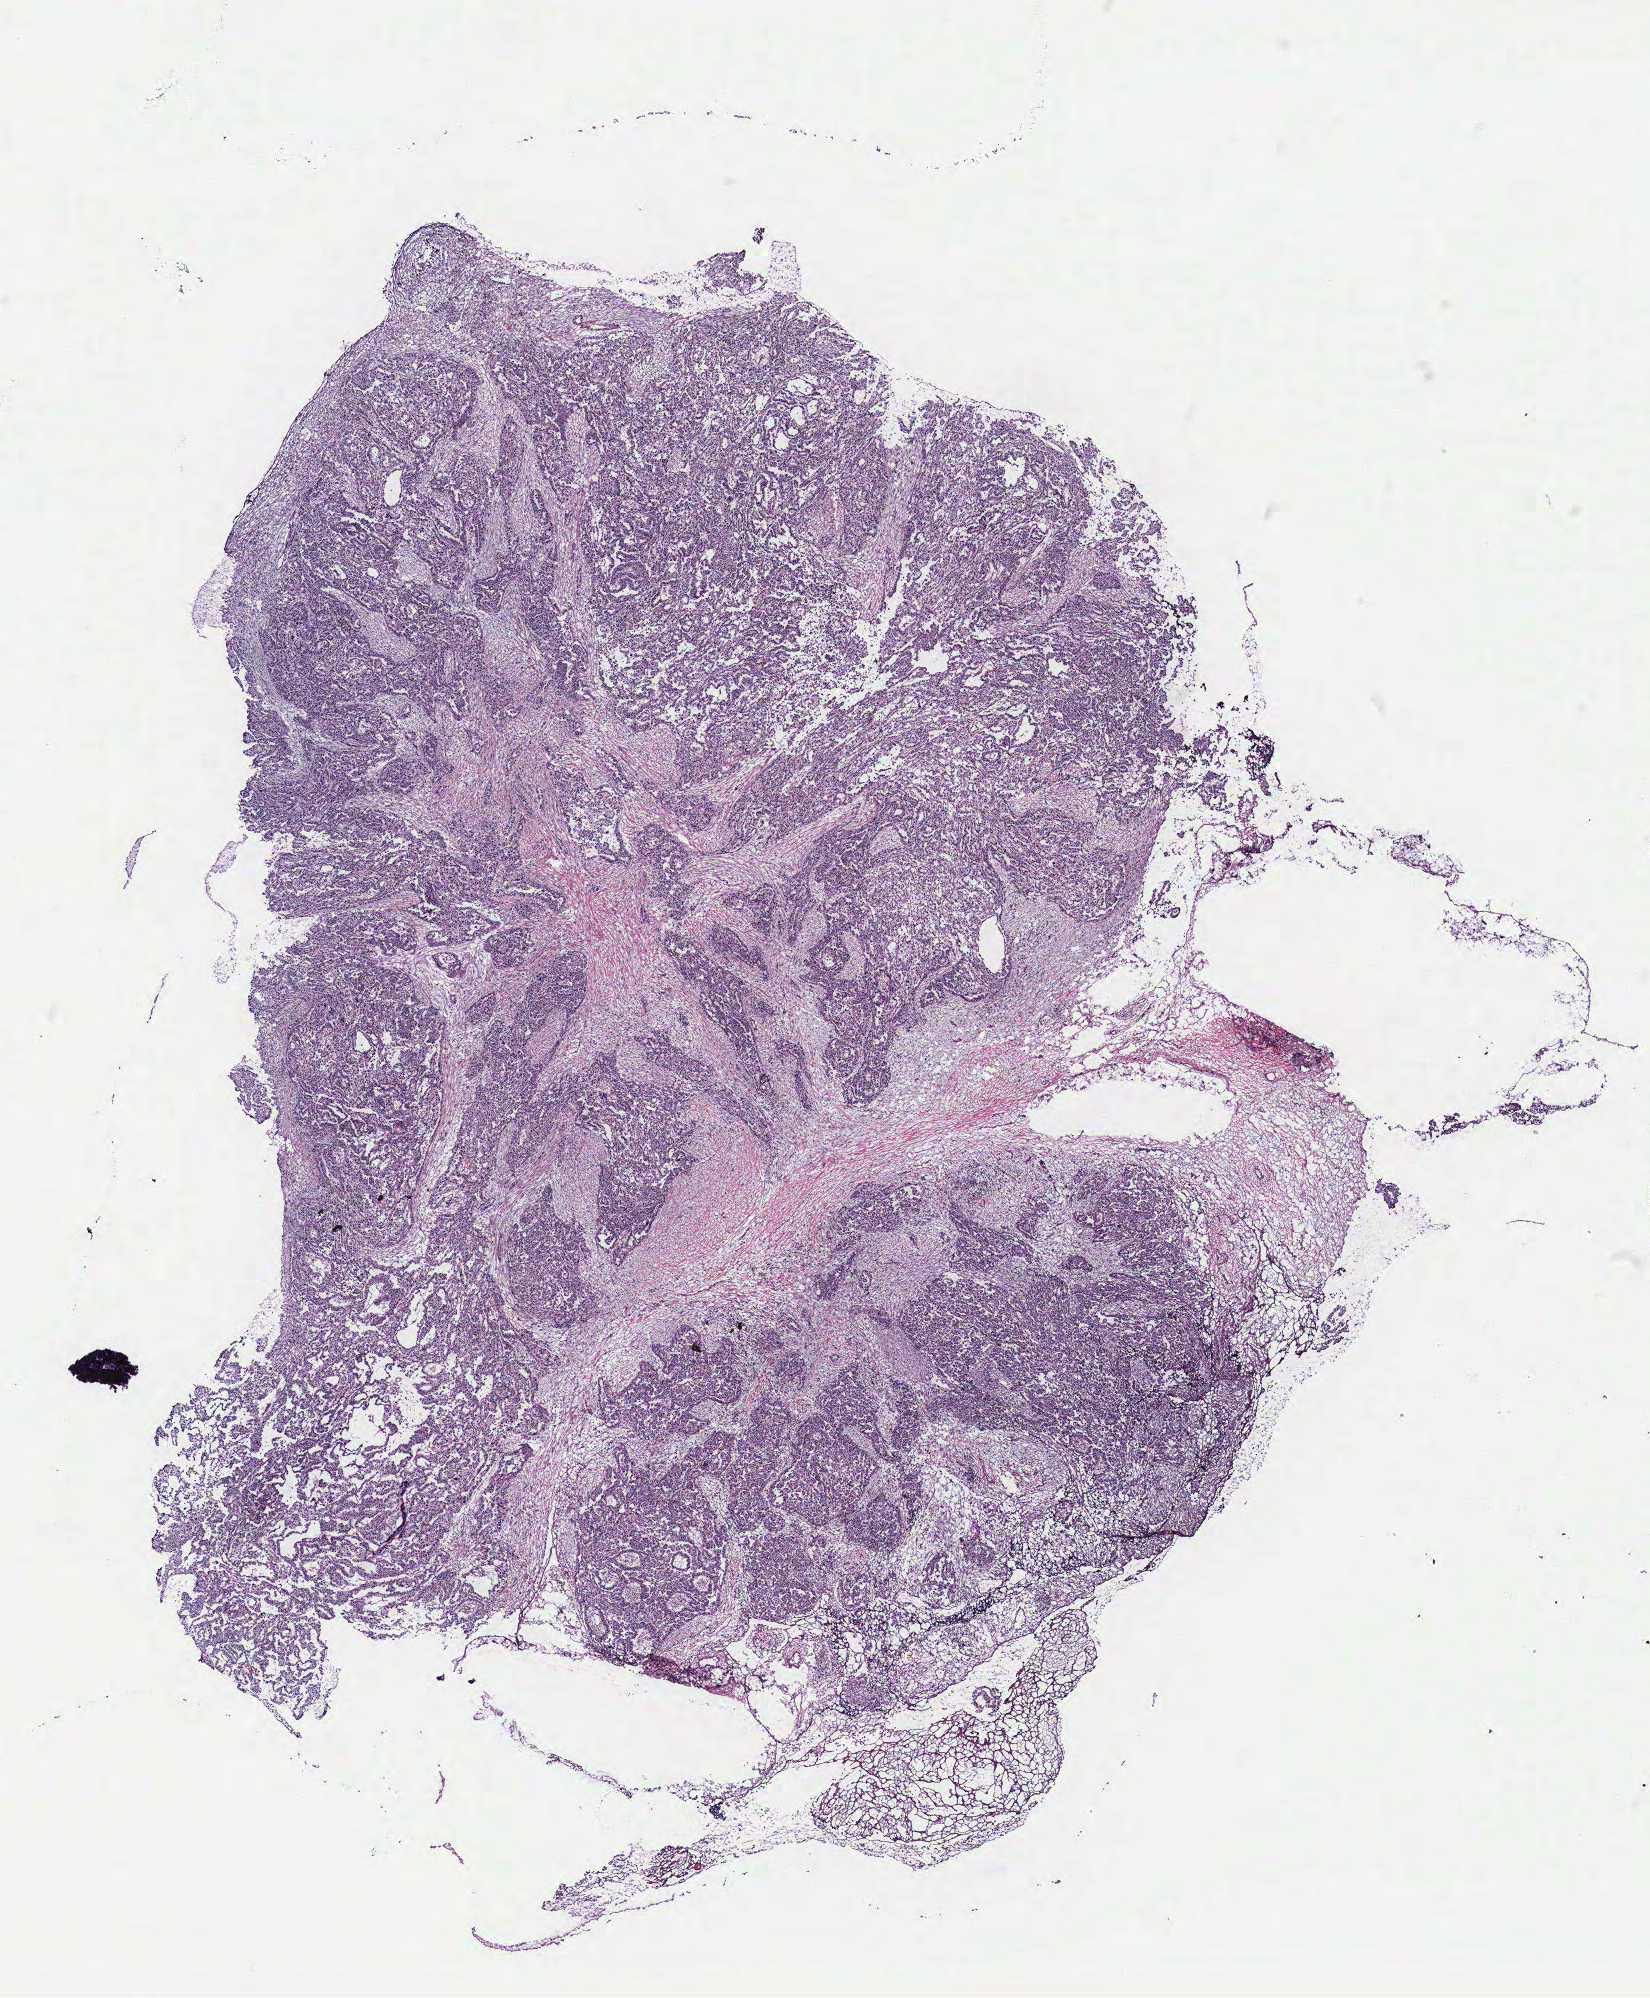
Whole-slide histology image, H&E-stained — shown as a low-resolution overview of the whole scanned area (about 13.2 x 16.0 mm, acquisition: 40x scan); ovary, tumour tissue. Female, 53 y/o.
Primary tumour site (as recorded): fallopian tube. Histologic diagnosis: Serous adenocarcinoma, NOS (fallopian tube).